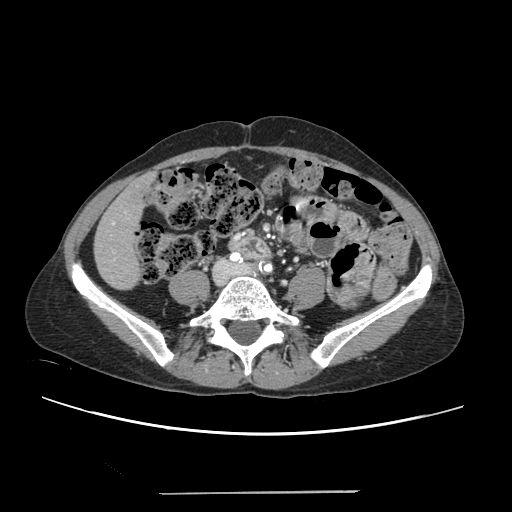
Contrast-enhanced abdominal CT, one axial slice; position 32 of 240 along the scan axis; 120 kVp; intravenous contrast given; soft-tissue window (W 400 / L 40 HU); 1.25 mm slice thickness; 512 × 512 image matrix, field of view 371 × 371 mm. Female patient, age 60 years. From the clinical record (not read from this slice): diagnosis: colorectal cancer liver metastases, imaged before liver resection; multiple liver metastases: no; largest metastasis: 1.5 cm; chemotherapy before resection: yes.
Outlined on this slice (expert manual segmentation):
- liver: bounding box (x1, y1, x2, y2) in pixels: (95, 177, 150, 289)
- planned liver remnant (the part of the liver to remain after resection): (95, 177, 150, 289)
- portal vein (with intrahepatic branches): (111, 222, 115, 259)